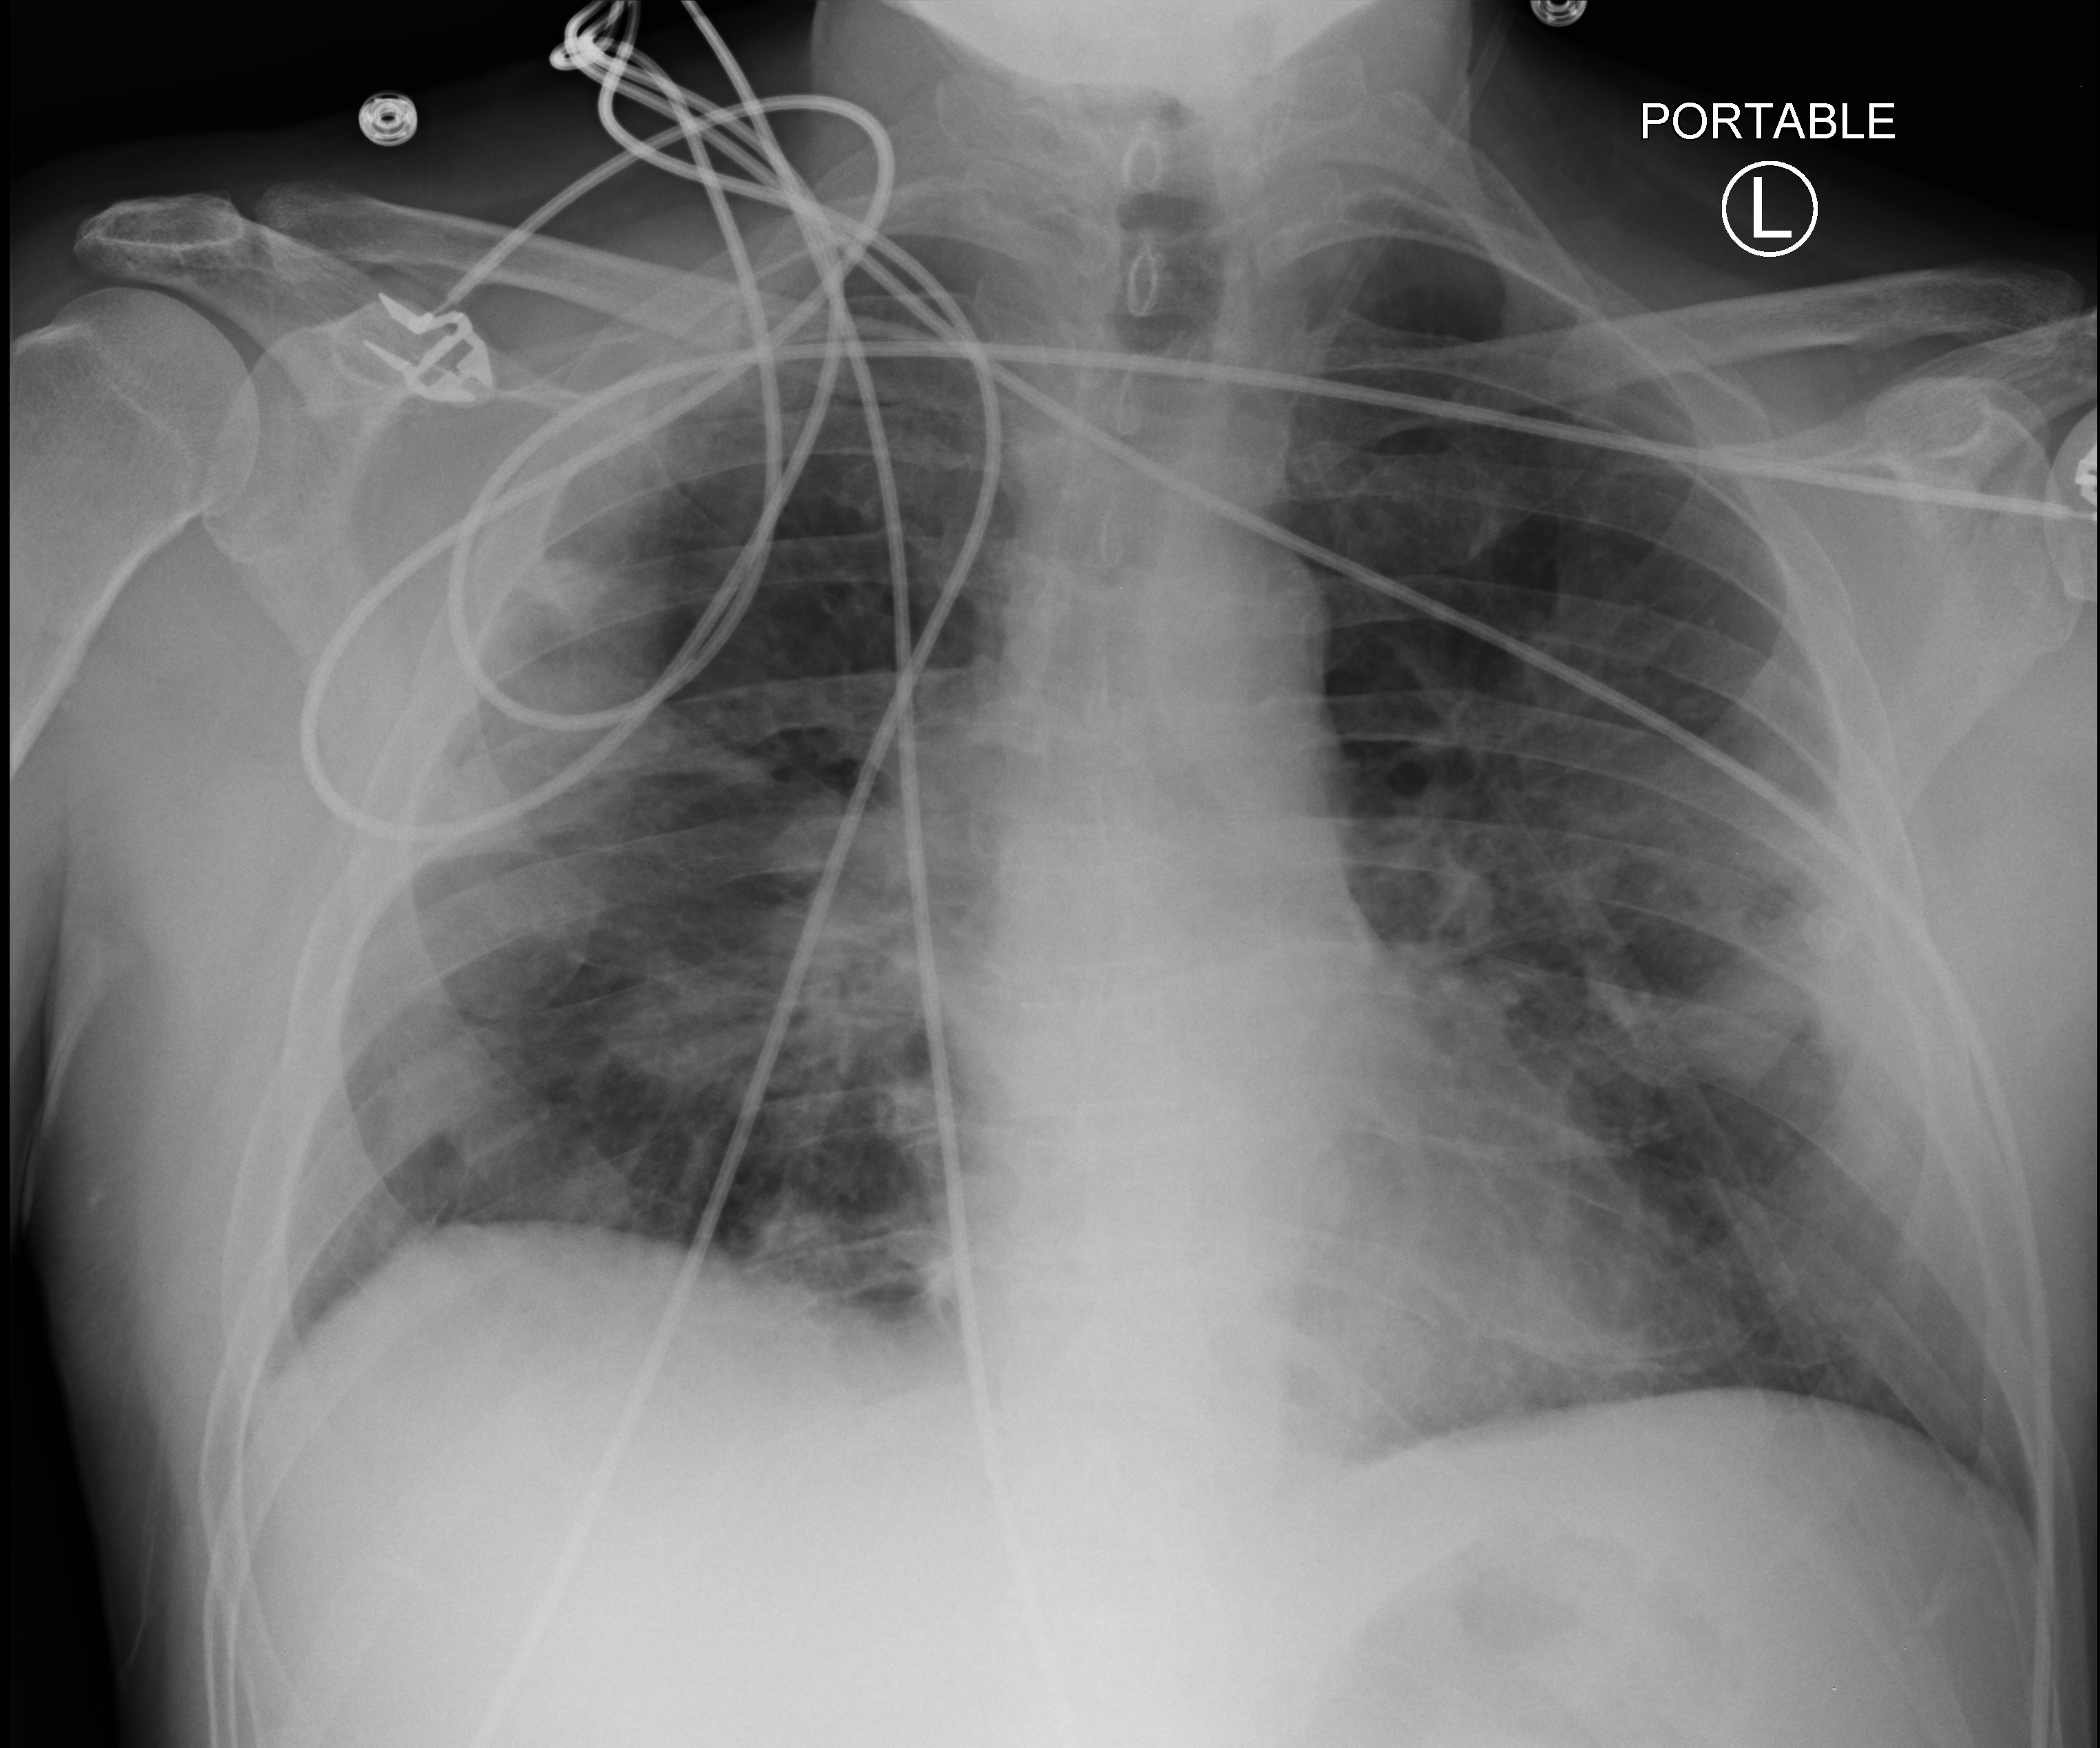
Chest X-ray (portable), anteroposterior (AP) projection. Patient hospitalised with COVID-19; male, aged 18–59 years.
Admission-level facts for this patient (not findings on this image; timing relative to this image not recorded): smoking status (admission record): former; admitted to intensive care during this hospital stay: no.